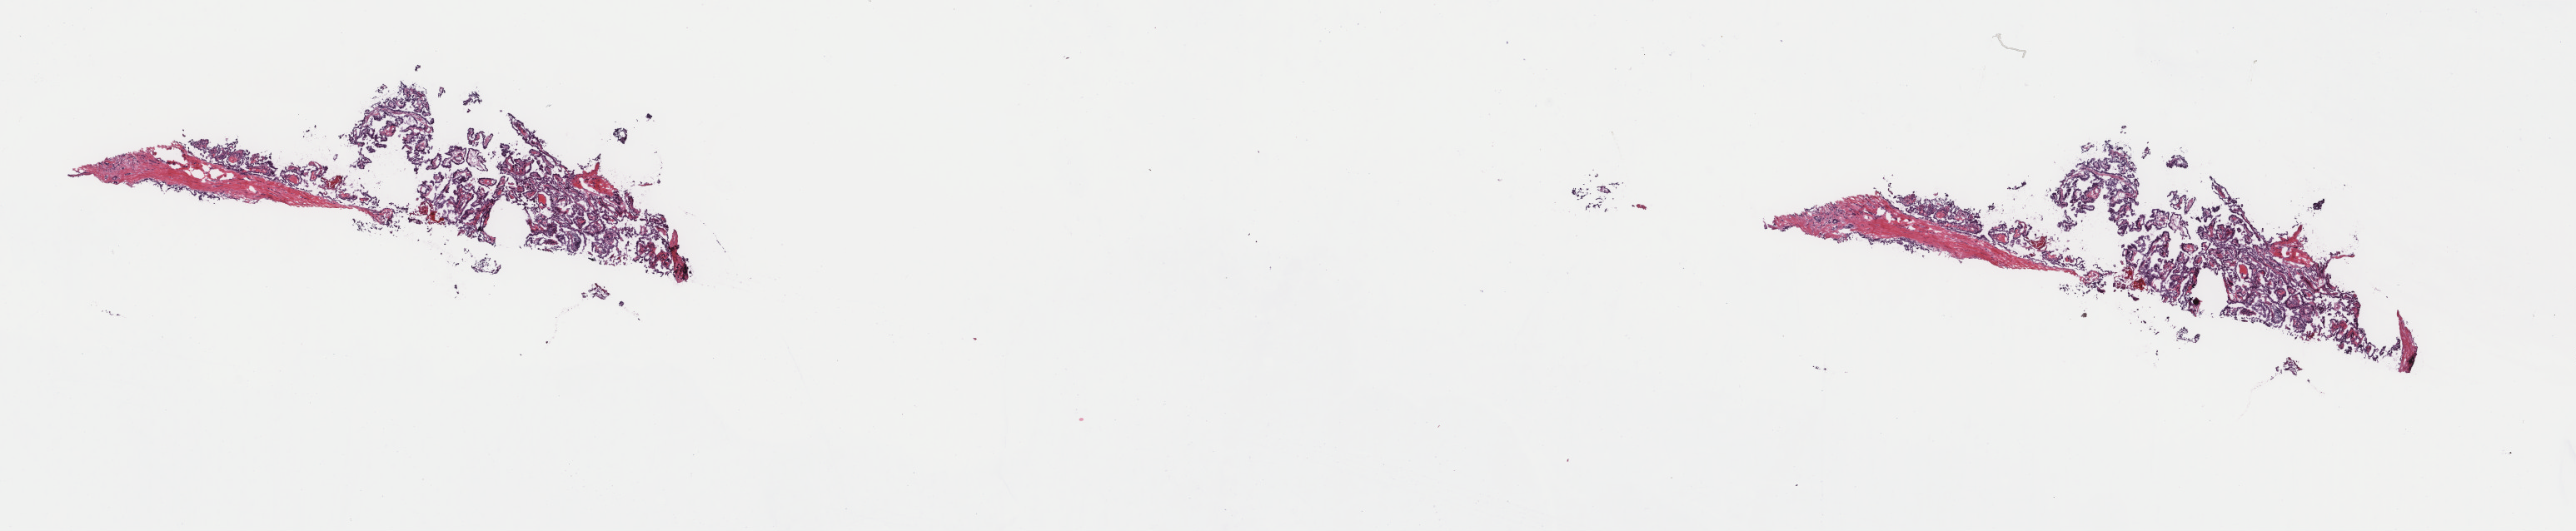
Digitized Hematoxylin and eosin (H&E) stained tissue section (whole slide), whole scanned area (about 24.6 x 5.1 mm) shown as a low-resolution overview. Frozen section. Thyroid, primary tumour sample. Patient: male, age at initial diagnosis 37 years. Composition of this section per pathologist review: tumour cells 85%, tumour nuclei 85%, normal cells 0%, stromal cells 15%, necrosis 0%. Inflammatory infiltration, as recorded: lymphocyte infiltration 2%, monocyte infiltration 0%, neutrophil infiltration 0%.
AJCC pathologic stage: I (7th edition). Lymph nodes positive (case pathology): 9 of 11 examined. Laterality: right. Histologic diagnosis: Nonencapsulated sclerosing carcinoma (thyroid gland).